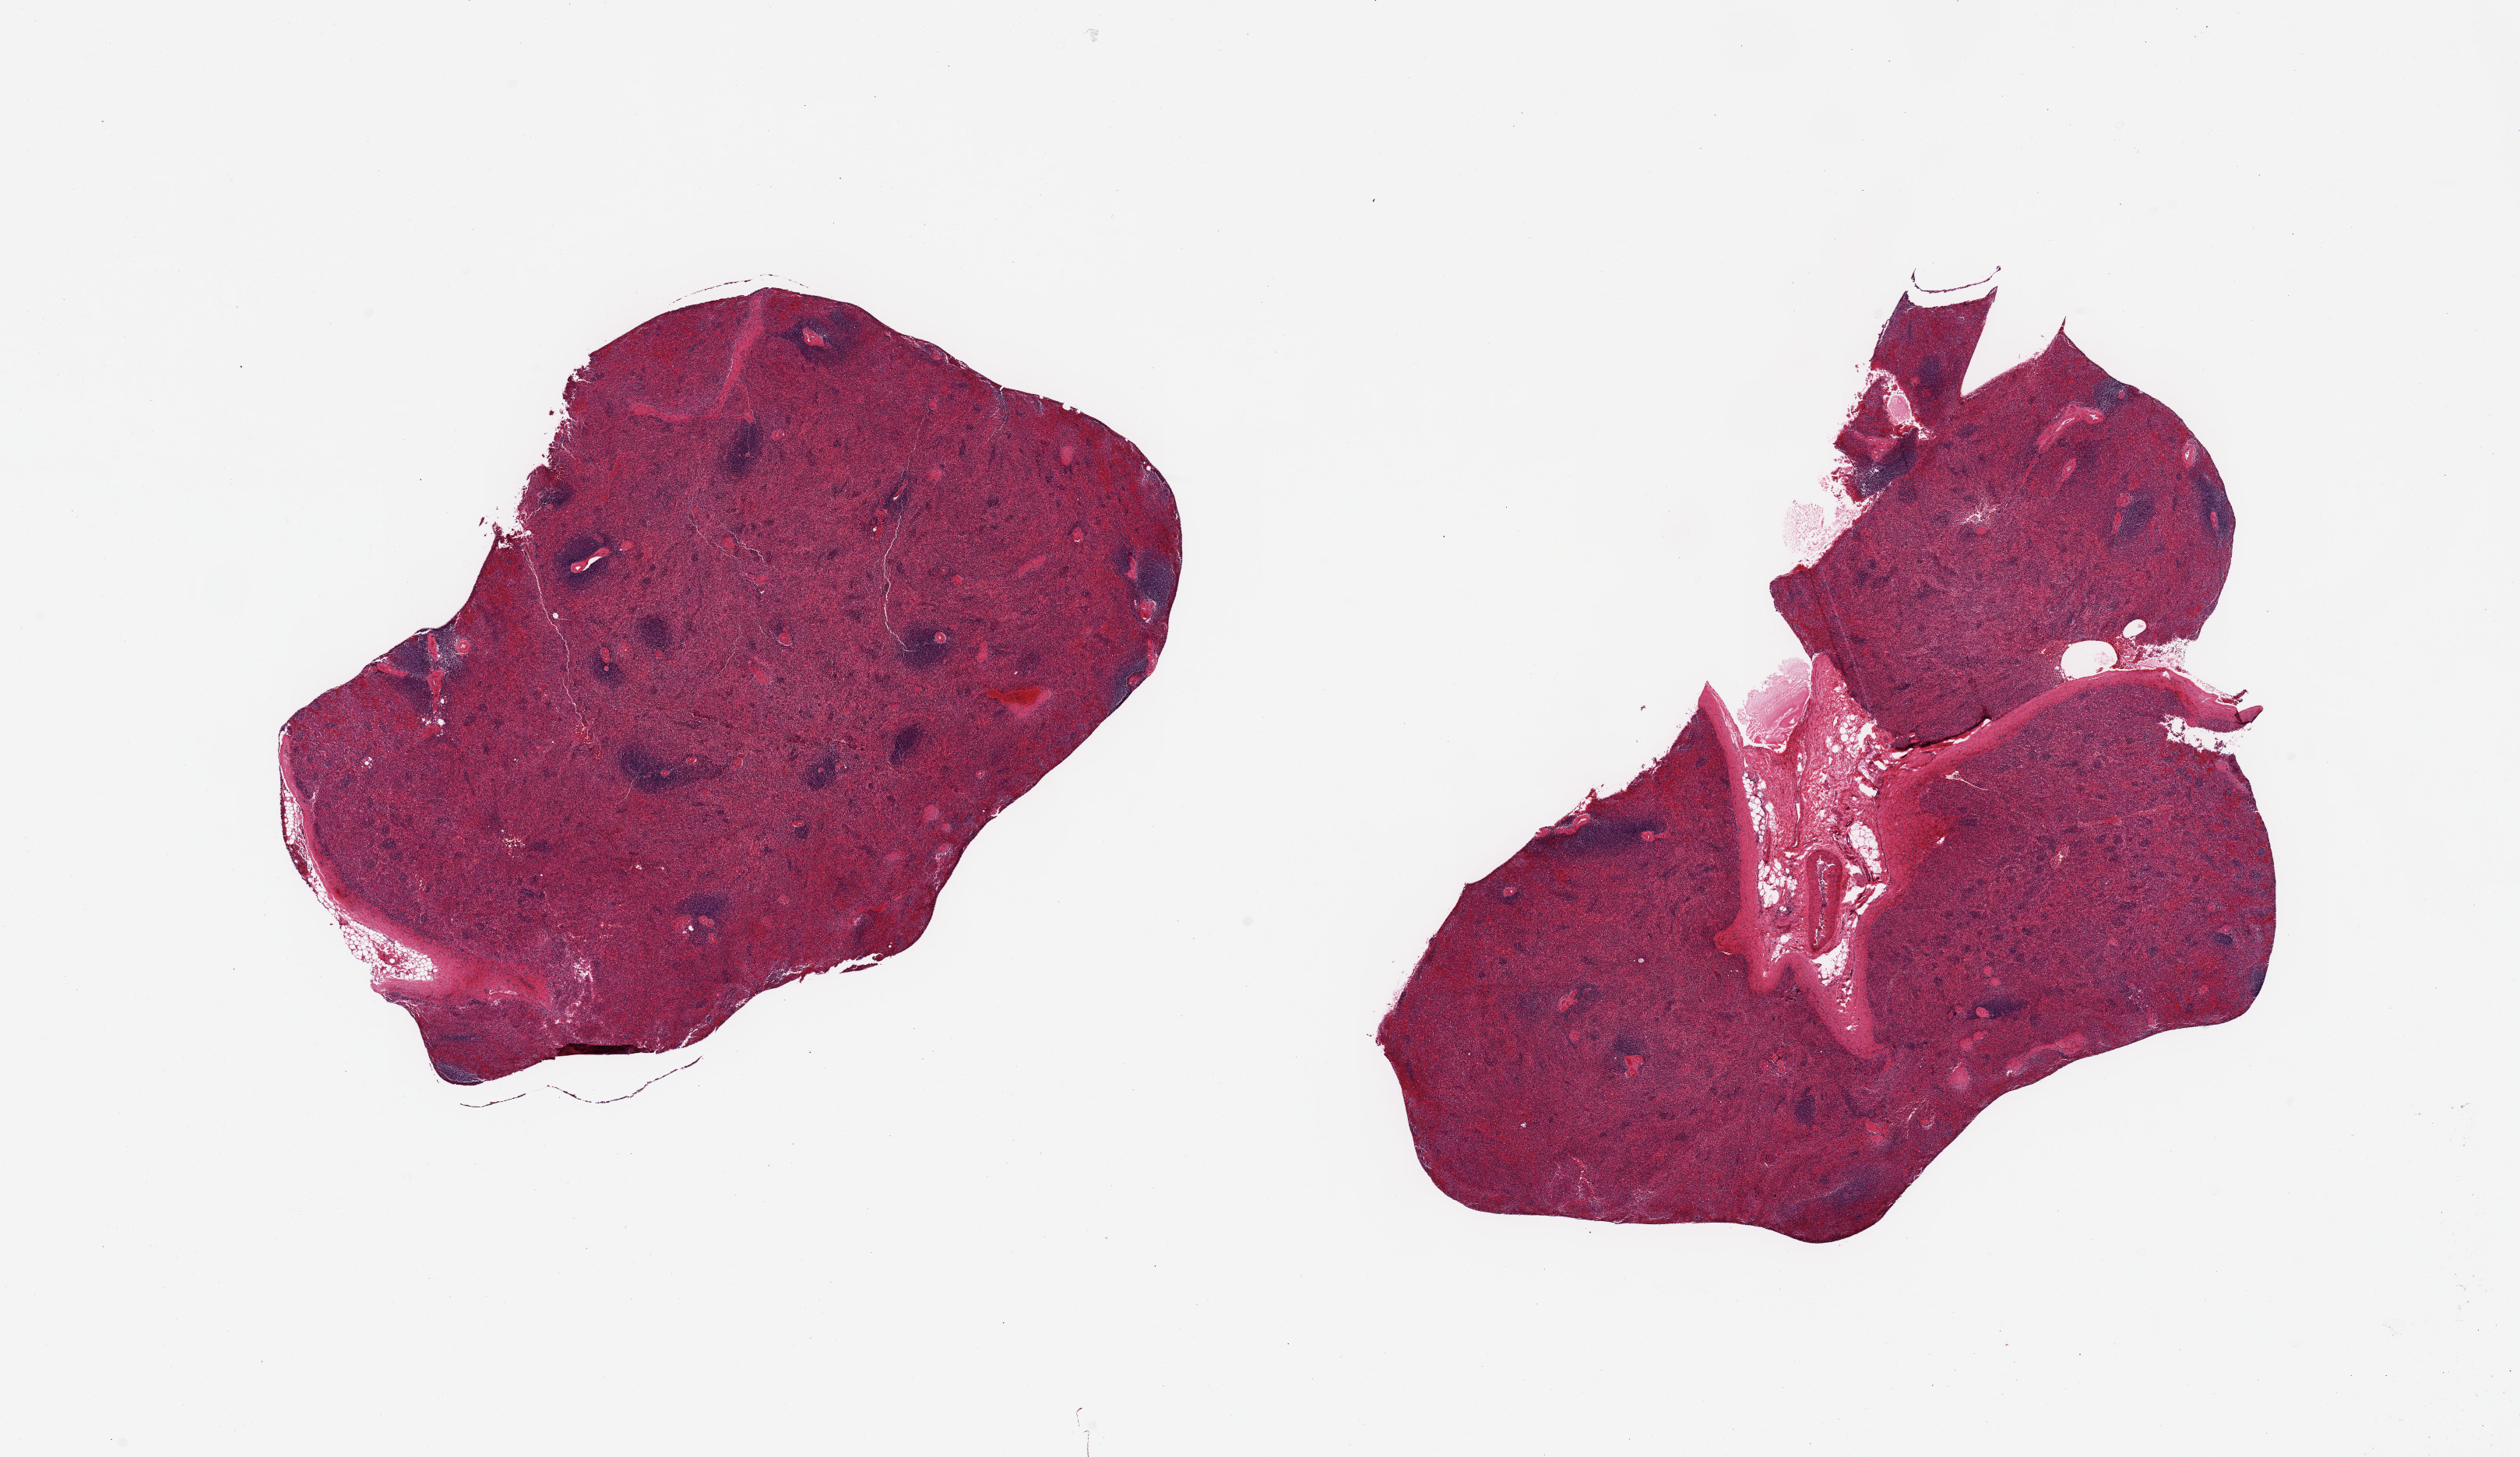
Haematoxylin and eosin whole-slide image, shown as a low-resolution overview of the whole scanned area (about 25.6 x 14.8 mm). PAXgene-fixed paraffin-embedded (PFPE) section. Section of spleen (target tissue). Tissue donor sample. Donor sex: female.
- reviewer comment on this tissue sample: 2 pieces, hilar vascular elements/fat up to ~10% of tissue